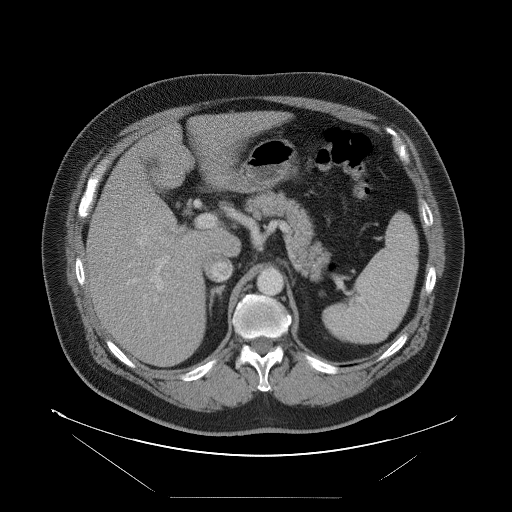
Contrast-enhanced abdominal CT, one axial slice. Slice 58 of 114 in the series (ordered by position). Intravenous contrast given. Soft-tissue window (W 400 / L 40 HU). 5 mm slice thickness. 512 × 512 image matrix, field of view 500 × 500 mm. Male patient, age 61 years. From the clinical record (not read from this slice): diagnosis: colorectal cancer liver metastases, imaged before liver resection; multiple liver metastases: no; largest metastasis: 6.5 cm.
Annotated regions visible in this slice (outlined manually by an expert reader):
- hepatic veins: bounding box (x1, y1, x2, y2) in pixels: (136, 231, 154, 246)
- liver: (88, 112, 278, 366)
- planned liver remnant (the part of the liver to remain after resection): (145, 112, 279, 237)
- portal vein (with intrahepatic branches): (150, 214, 211, 302)